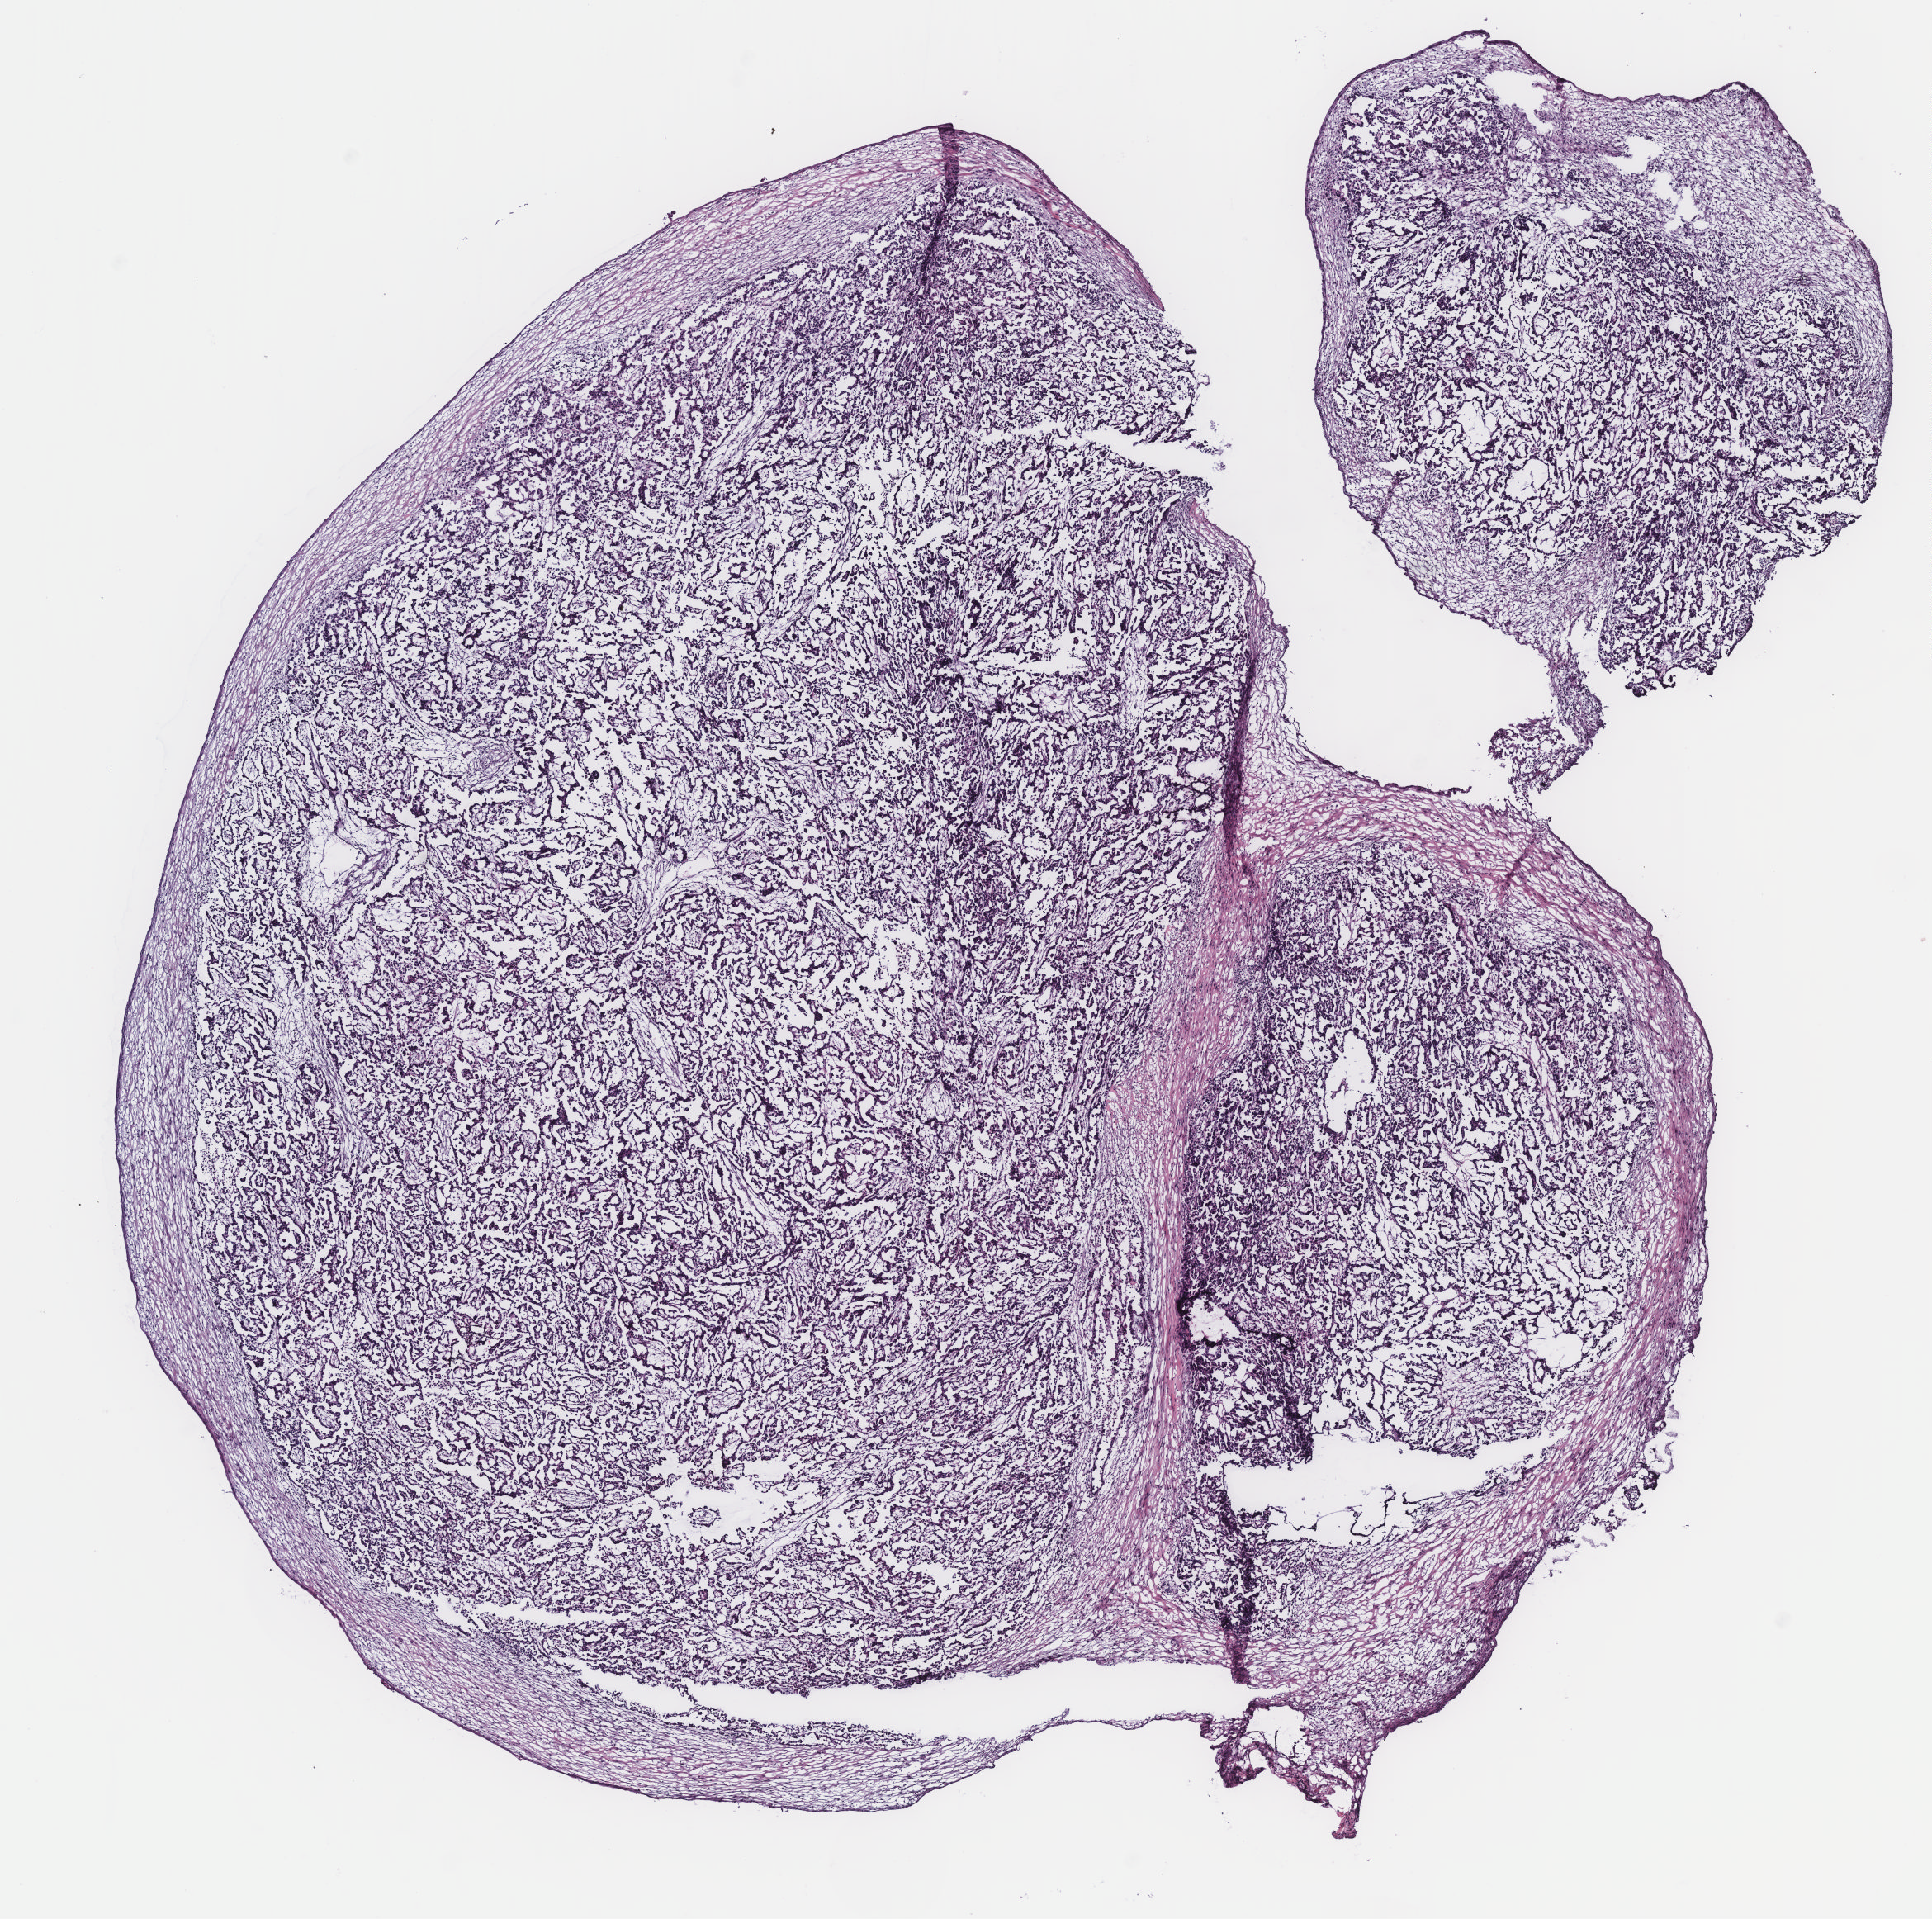
H&E-stained whole-slide image — low-resolution overview of the scanned area, about 9.4 x 9.3 mm (slide scanned at 40x). Ovary, tissue type not recorded. Patient sex: female.
Patient diagnosis: Serous adenocarcinoma, NOS.